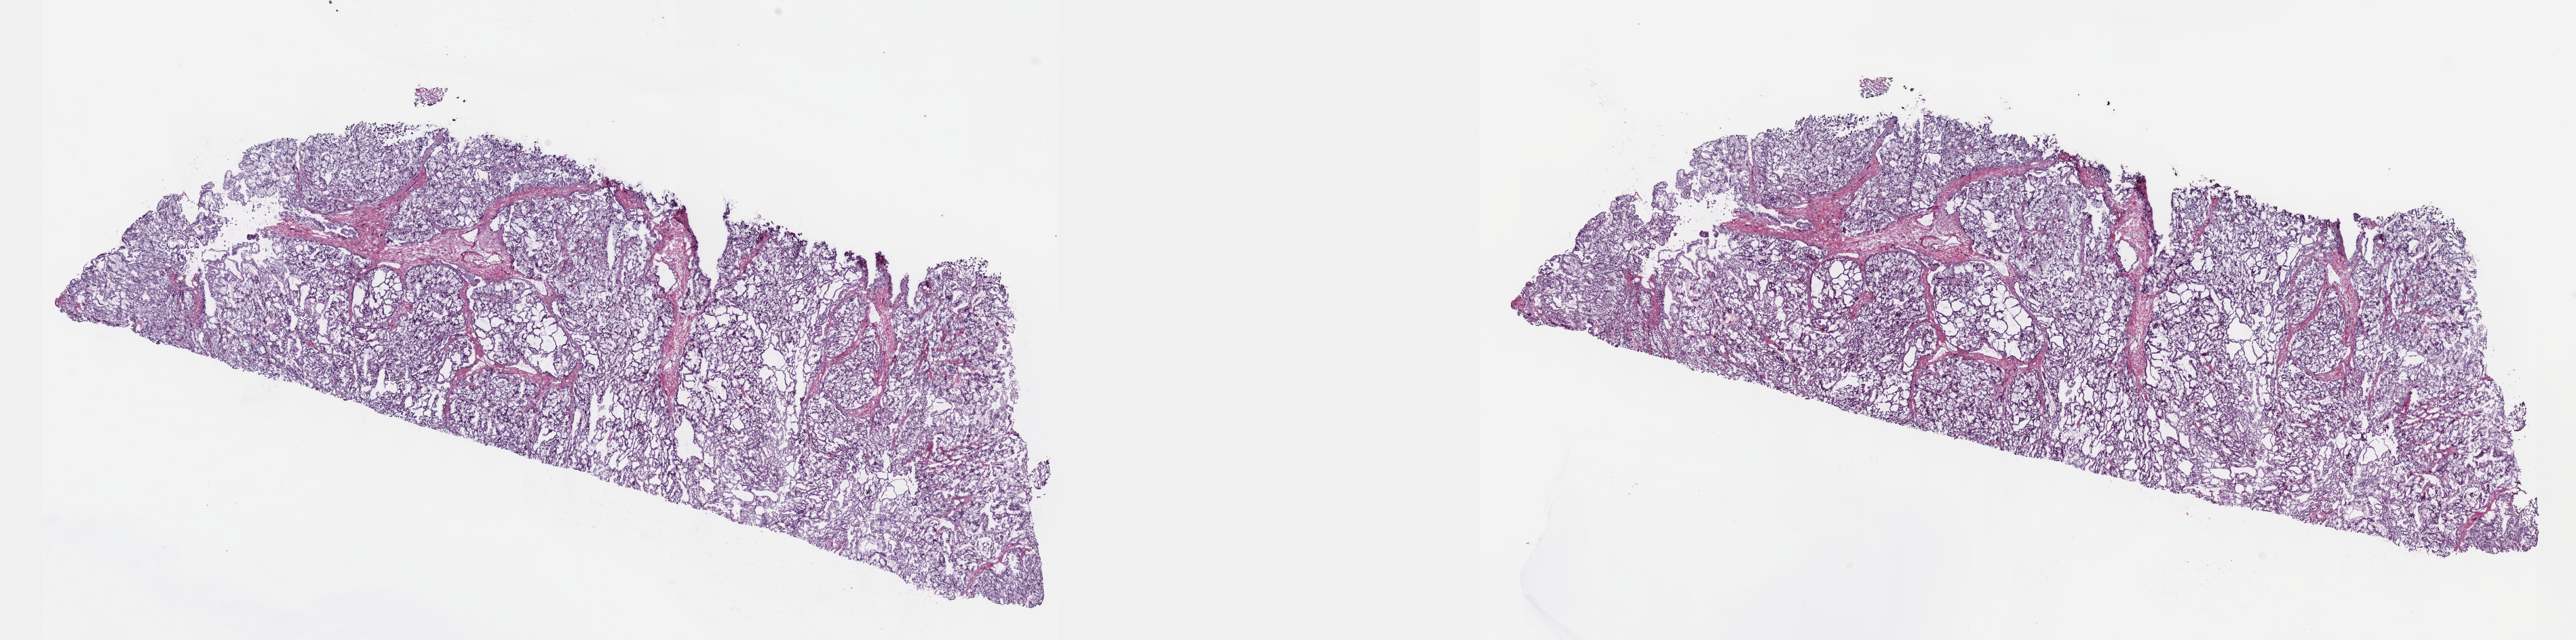
Whole-slide histology image, Hematoxylin and eosin (H&E) stained, a low-resolution overview of the entire scanned area, about 30.7 x 7.6 mm (acquisition: 40x scan); frozen section from the top of the tissue portion; kidney, primary tumour sample. Male, age 59 years at initial diagnosis. Slide review estimates, as recorded: tumour cells 80%, tumour nuclei 90%, normal cells 0%, stromal cells 20%, necrosis 0%. Inflammatory infiltration, as recorded: lymphocyte infiltration 0%, monocyte infiltration 0%, neutrophil infiltration 0%.
AJCC pathologic stage: III (6th edition). Histologic diagnosis: Papillary adenocarcinoma, NOS.